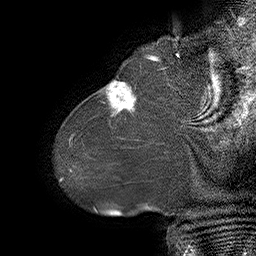
Breast MRI (dynamic contrast-enhanced), one sagittal slice; slice 8 of 55 in the series (ordered by position); dynamic contrast-enhanced series, time point 2 of 6 at this slice position (early post-contrast); 1.5 T; TE 4.5 ms, TR 32.4 ms; 256 × 256 image matrix, field of view 180 × 180 mm. Female patient. Case-level facts recorded for this patient, not image findings: setting: breast cancer imaged before/during neoadjuvant chemotherapy; receptor status: HER2-positive.
Outlined on this slice (semi-automatically segmented with operator editing):
- analysis volume of interest (the breast-tissue region the enhancement analysis was run in; not a lesion): bounding box [x1, y1, x2, y2] px = [80, 64, 163, 134]
- tumour enhancement mask (voxels above the 100 % enhancement threshold inside the analysis volume of interest): [105, 80, 136, 115]